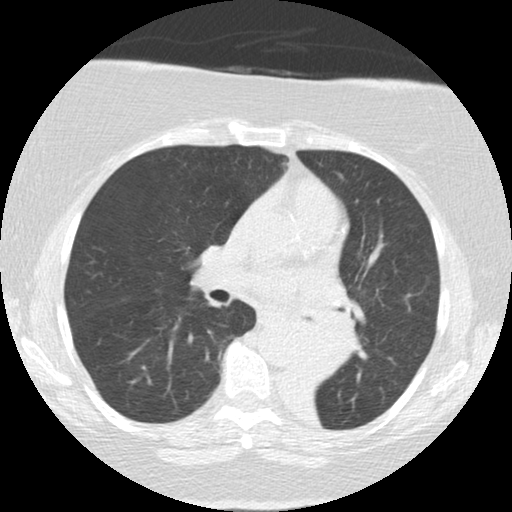
Low-dose screening chest CT, one axial slice. Slice 76 of 136 in the series (ordered by position). Reconstruction kernel STANDARD. Lung window (W 1500 / L -600 HU). 2.5 mm slice thickness. 512 × 512 image matrix.
Outlined on this slice (expert manual segmentation):
- lesion 2 (tumor, mediastinum): bounding box (x1, y1, x2, y2) in pixels: (290, 308, 359, 384)